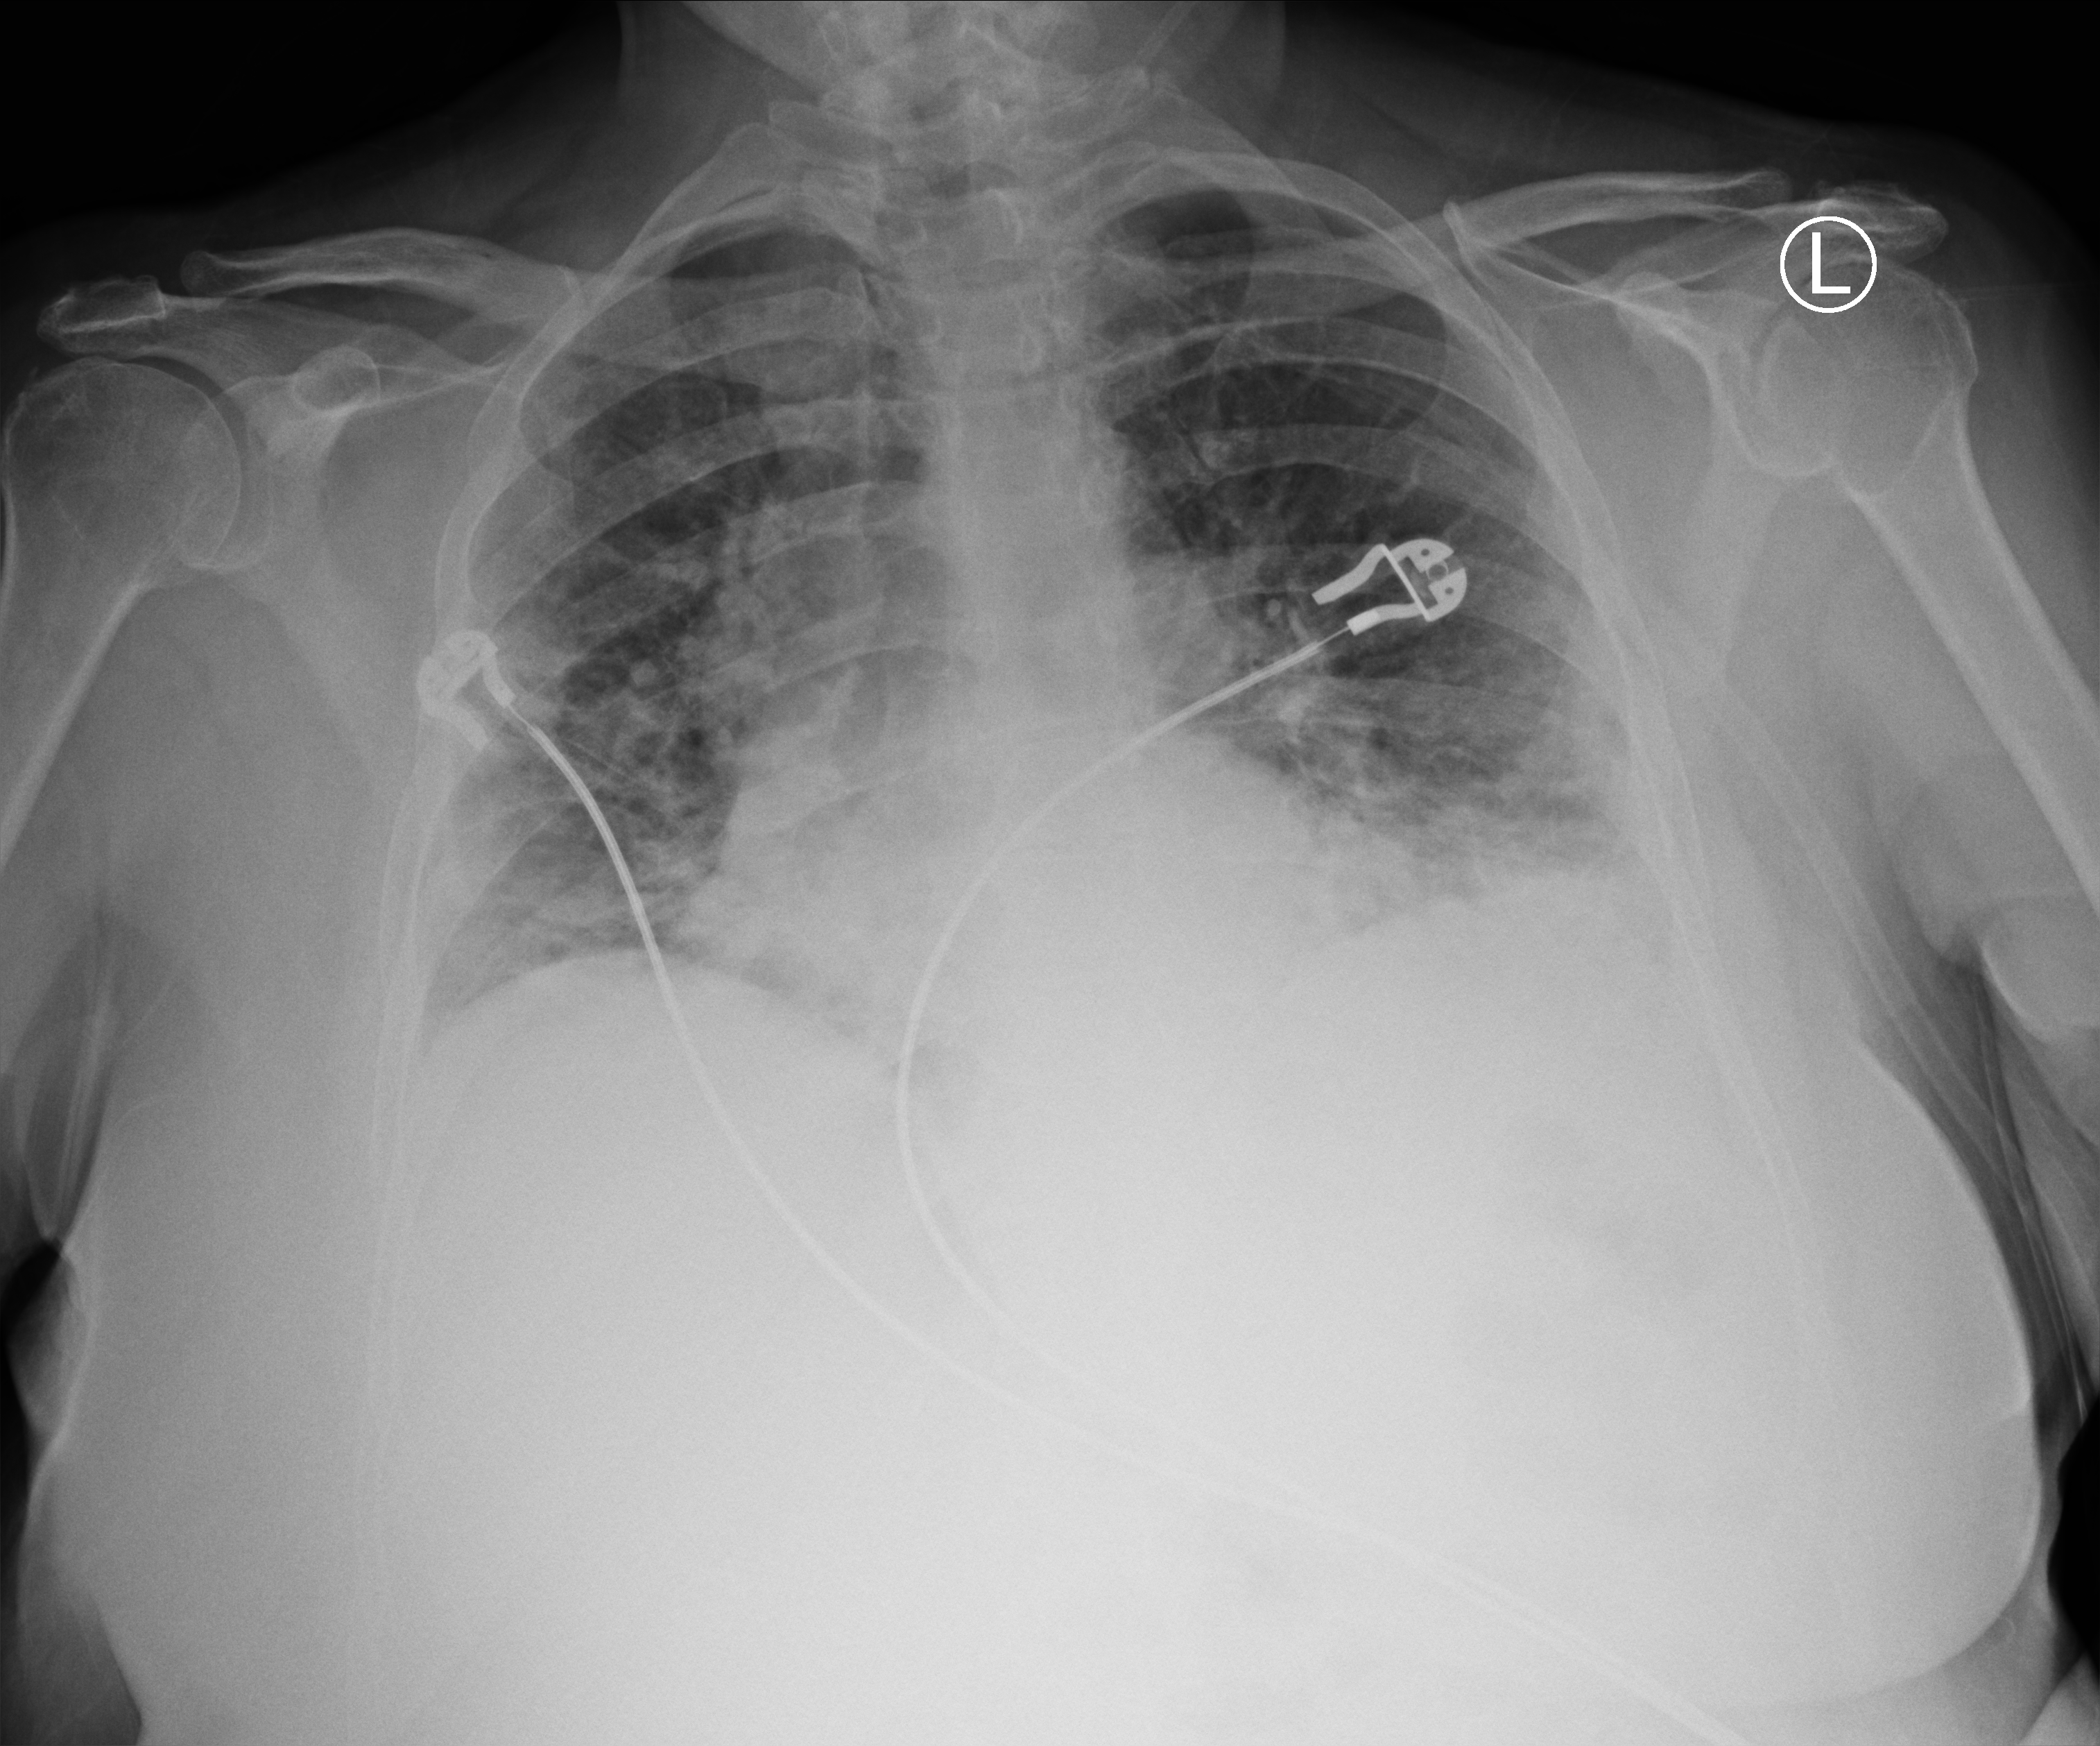
Bedside chest radiograph (computed radiography). Female patient hospitalised with COVID-19, age 60–74 years.
From the hospital-stay record, not from the radiograph (when in the stay this image was taken is not recorded):
- admitted to intensive care during this hospital stay: no